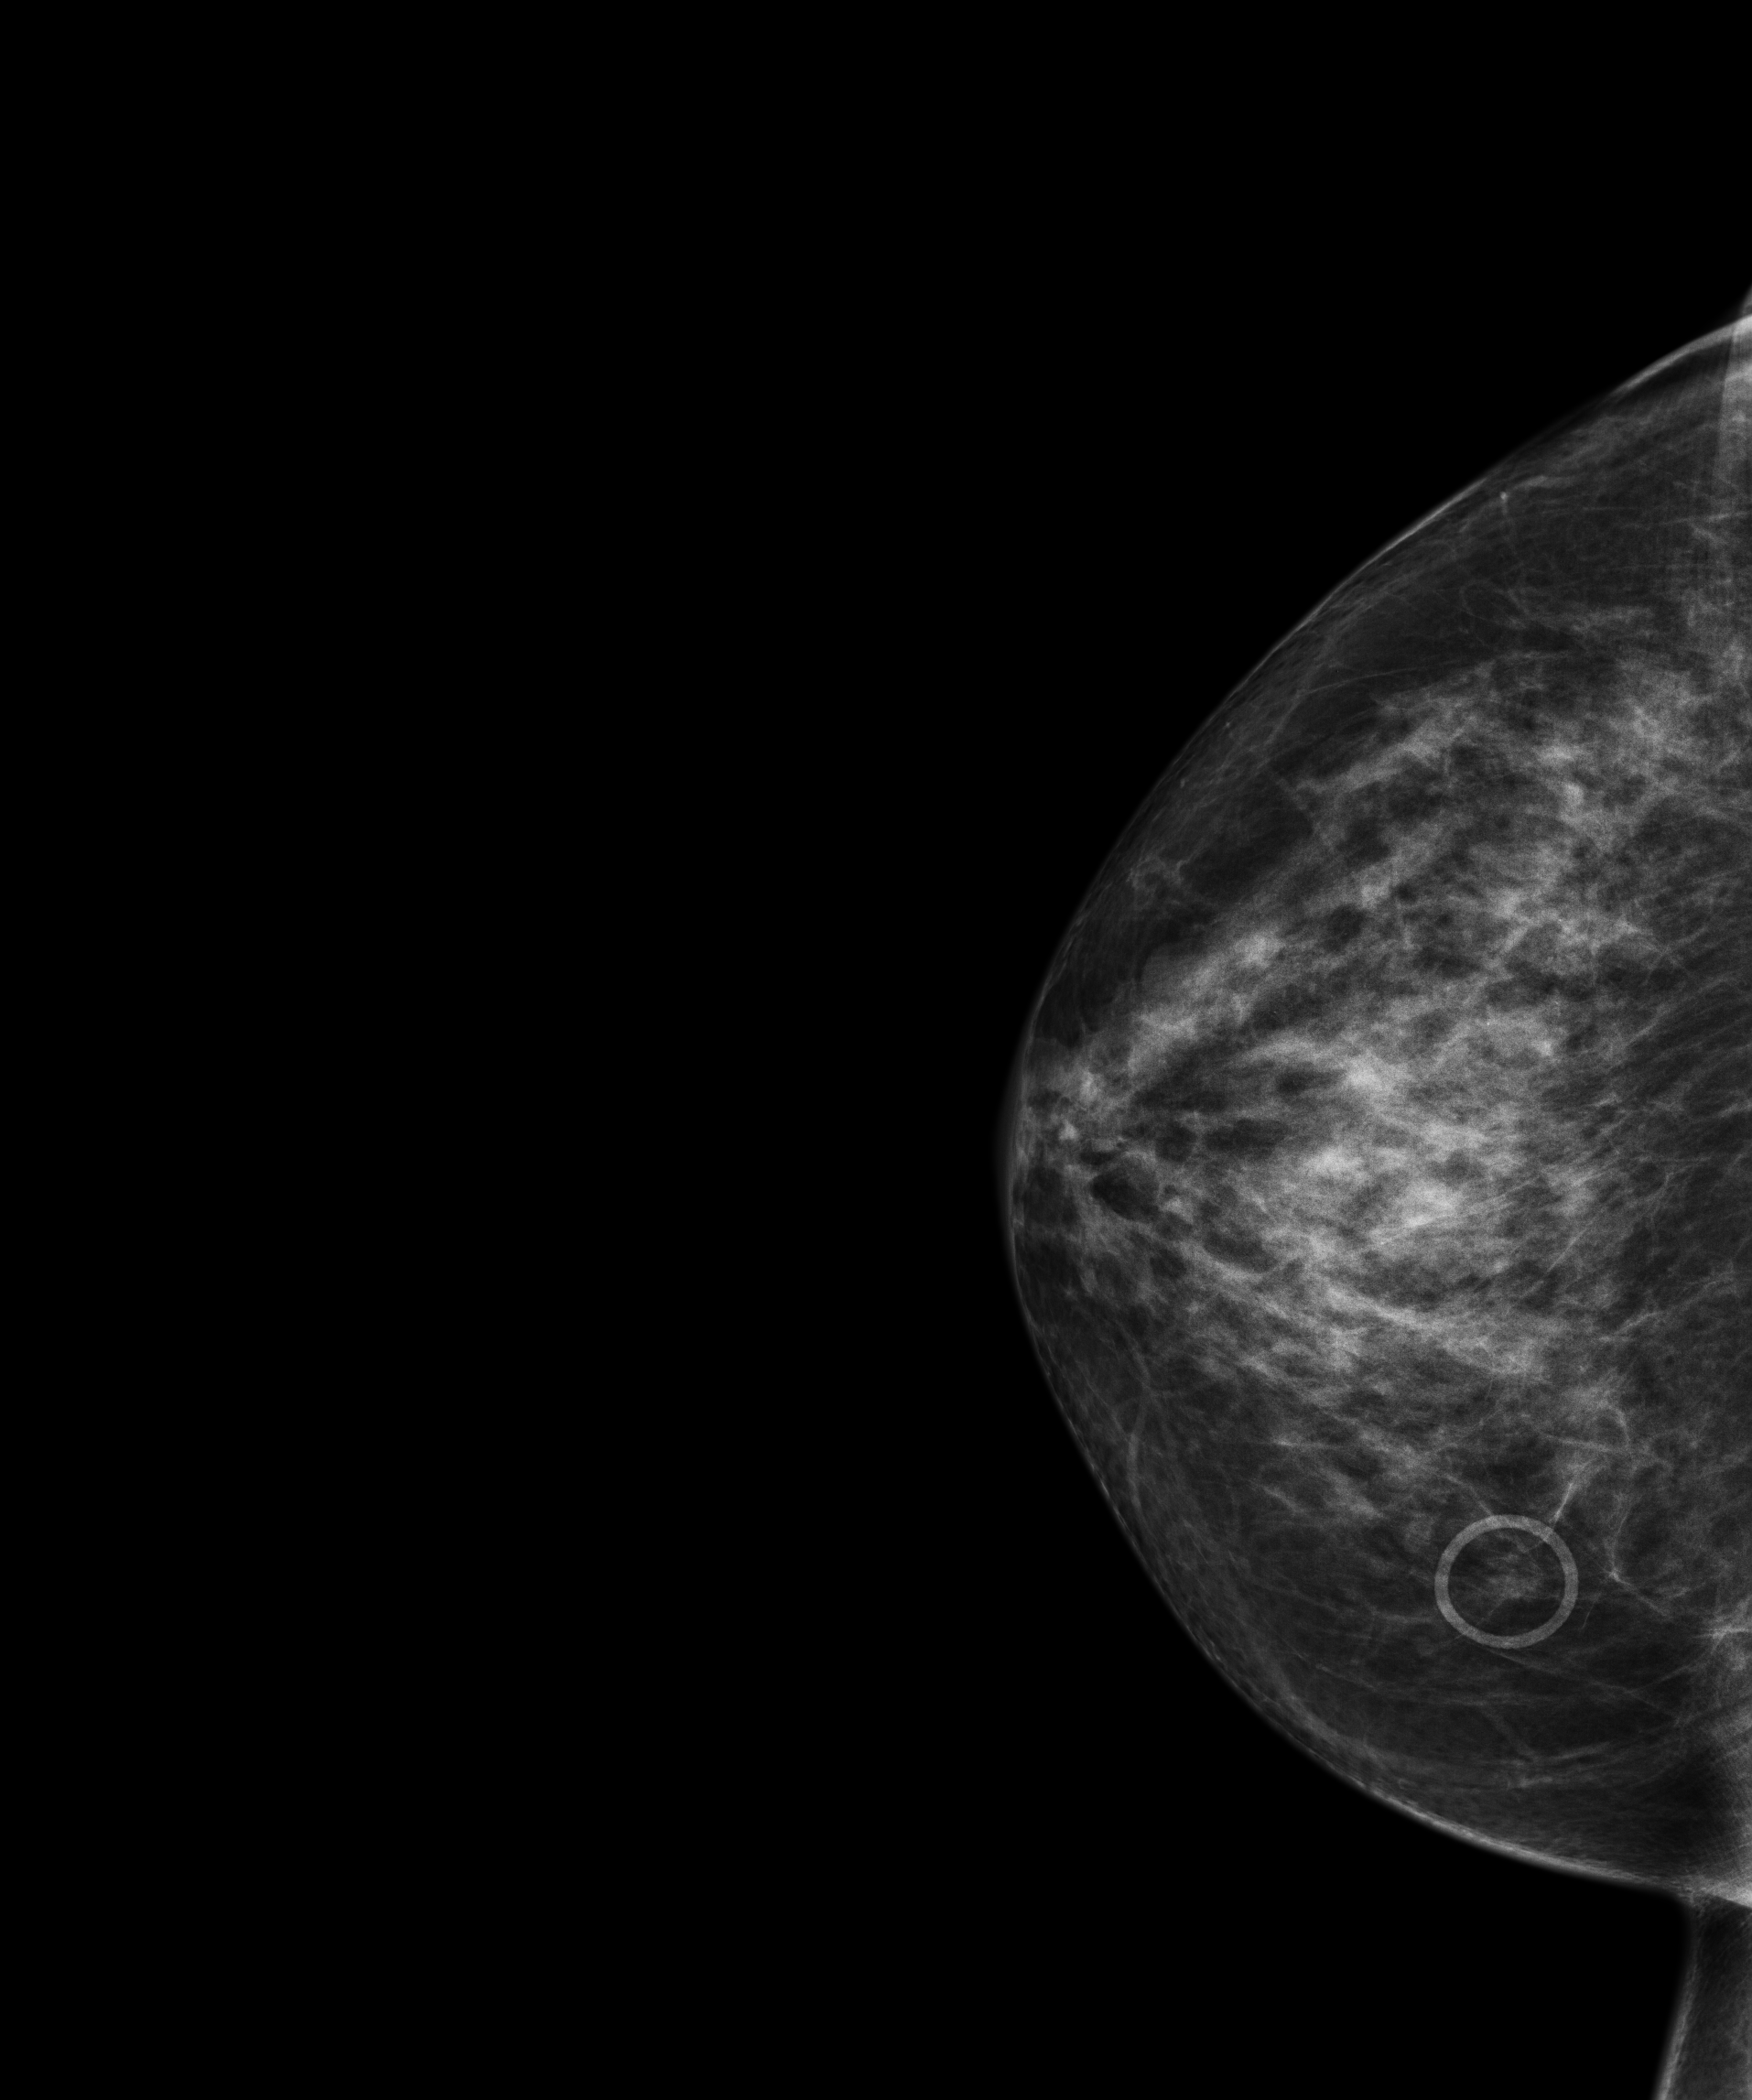
Full-field digital mammogram (FFDM), right breast, cranio-caudal projection, annual screening mammography examination, compressed breast thickness 64 mm, system: Senographe Essential ADS_56.21.3. Patient: female, 58 years.
- breast density at the screening exam (both breasts): heterogeneously dense (BI-RADS density category c)
- final BI-RADS assessment for this screening round (tomosynthesis exam, both breasts): category 1
- recall: no recall after this screen